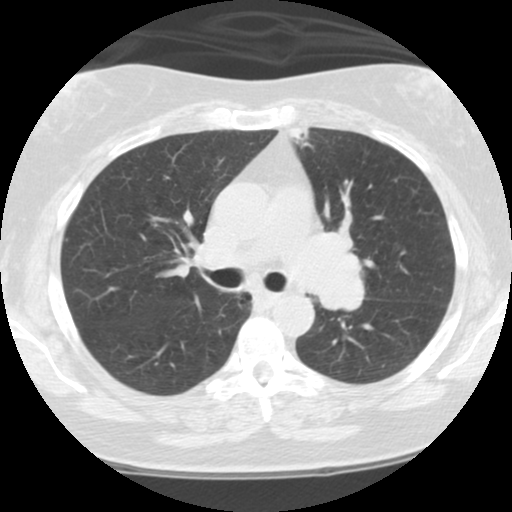
Low-dose screening chest CT, axial slice; third screening round (two years after baseline); lung window (W 1500 / L -600 HU); 2.5 mm slice thickness; 120 kVp; slice 40 of 108 in the series; 512 × 512 image matrix. Female, age 59 years at enrolment. Current smoker at enrolment.
Expert-annotated lung lesion, bounding box [x1, y1, x2, y2] px = [285, 213, 383, 325]. No non-calcified nodule or mass ≥4 mm was recorded by the screening reader at this exam. Official screen result: positive, other. Later outcome: lung cancer diagnosed 192 days after this screen — small cell carcinoma, NOS, left upper lobe, left hilum, mediastinum, left main stem bronchus, stage IV (AJCC 6th edition), 63 mm at pathology.